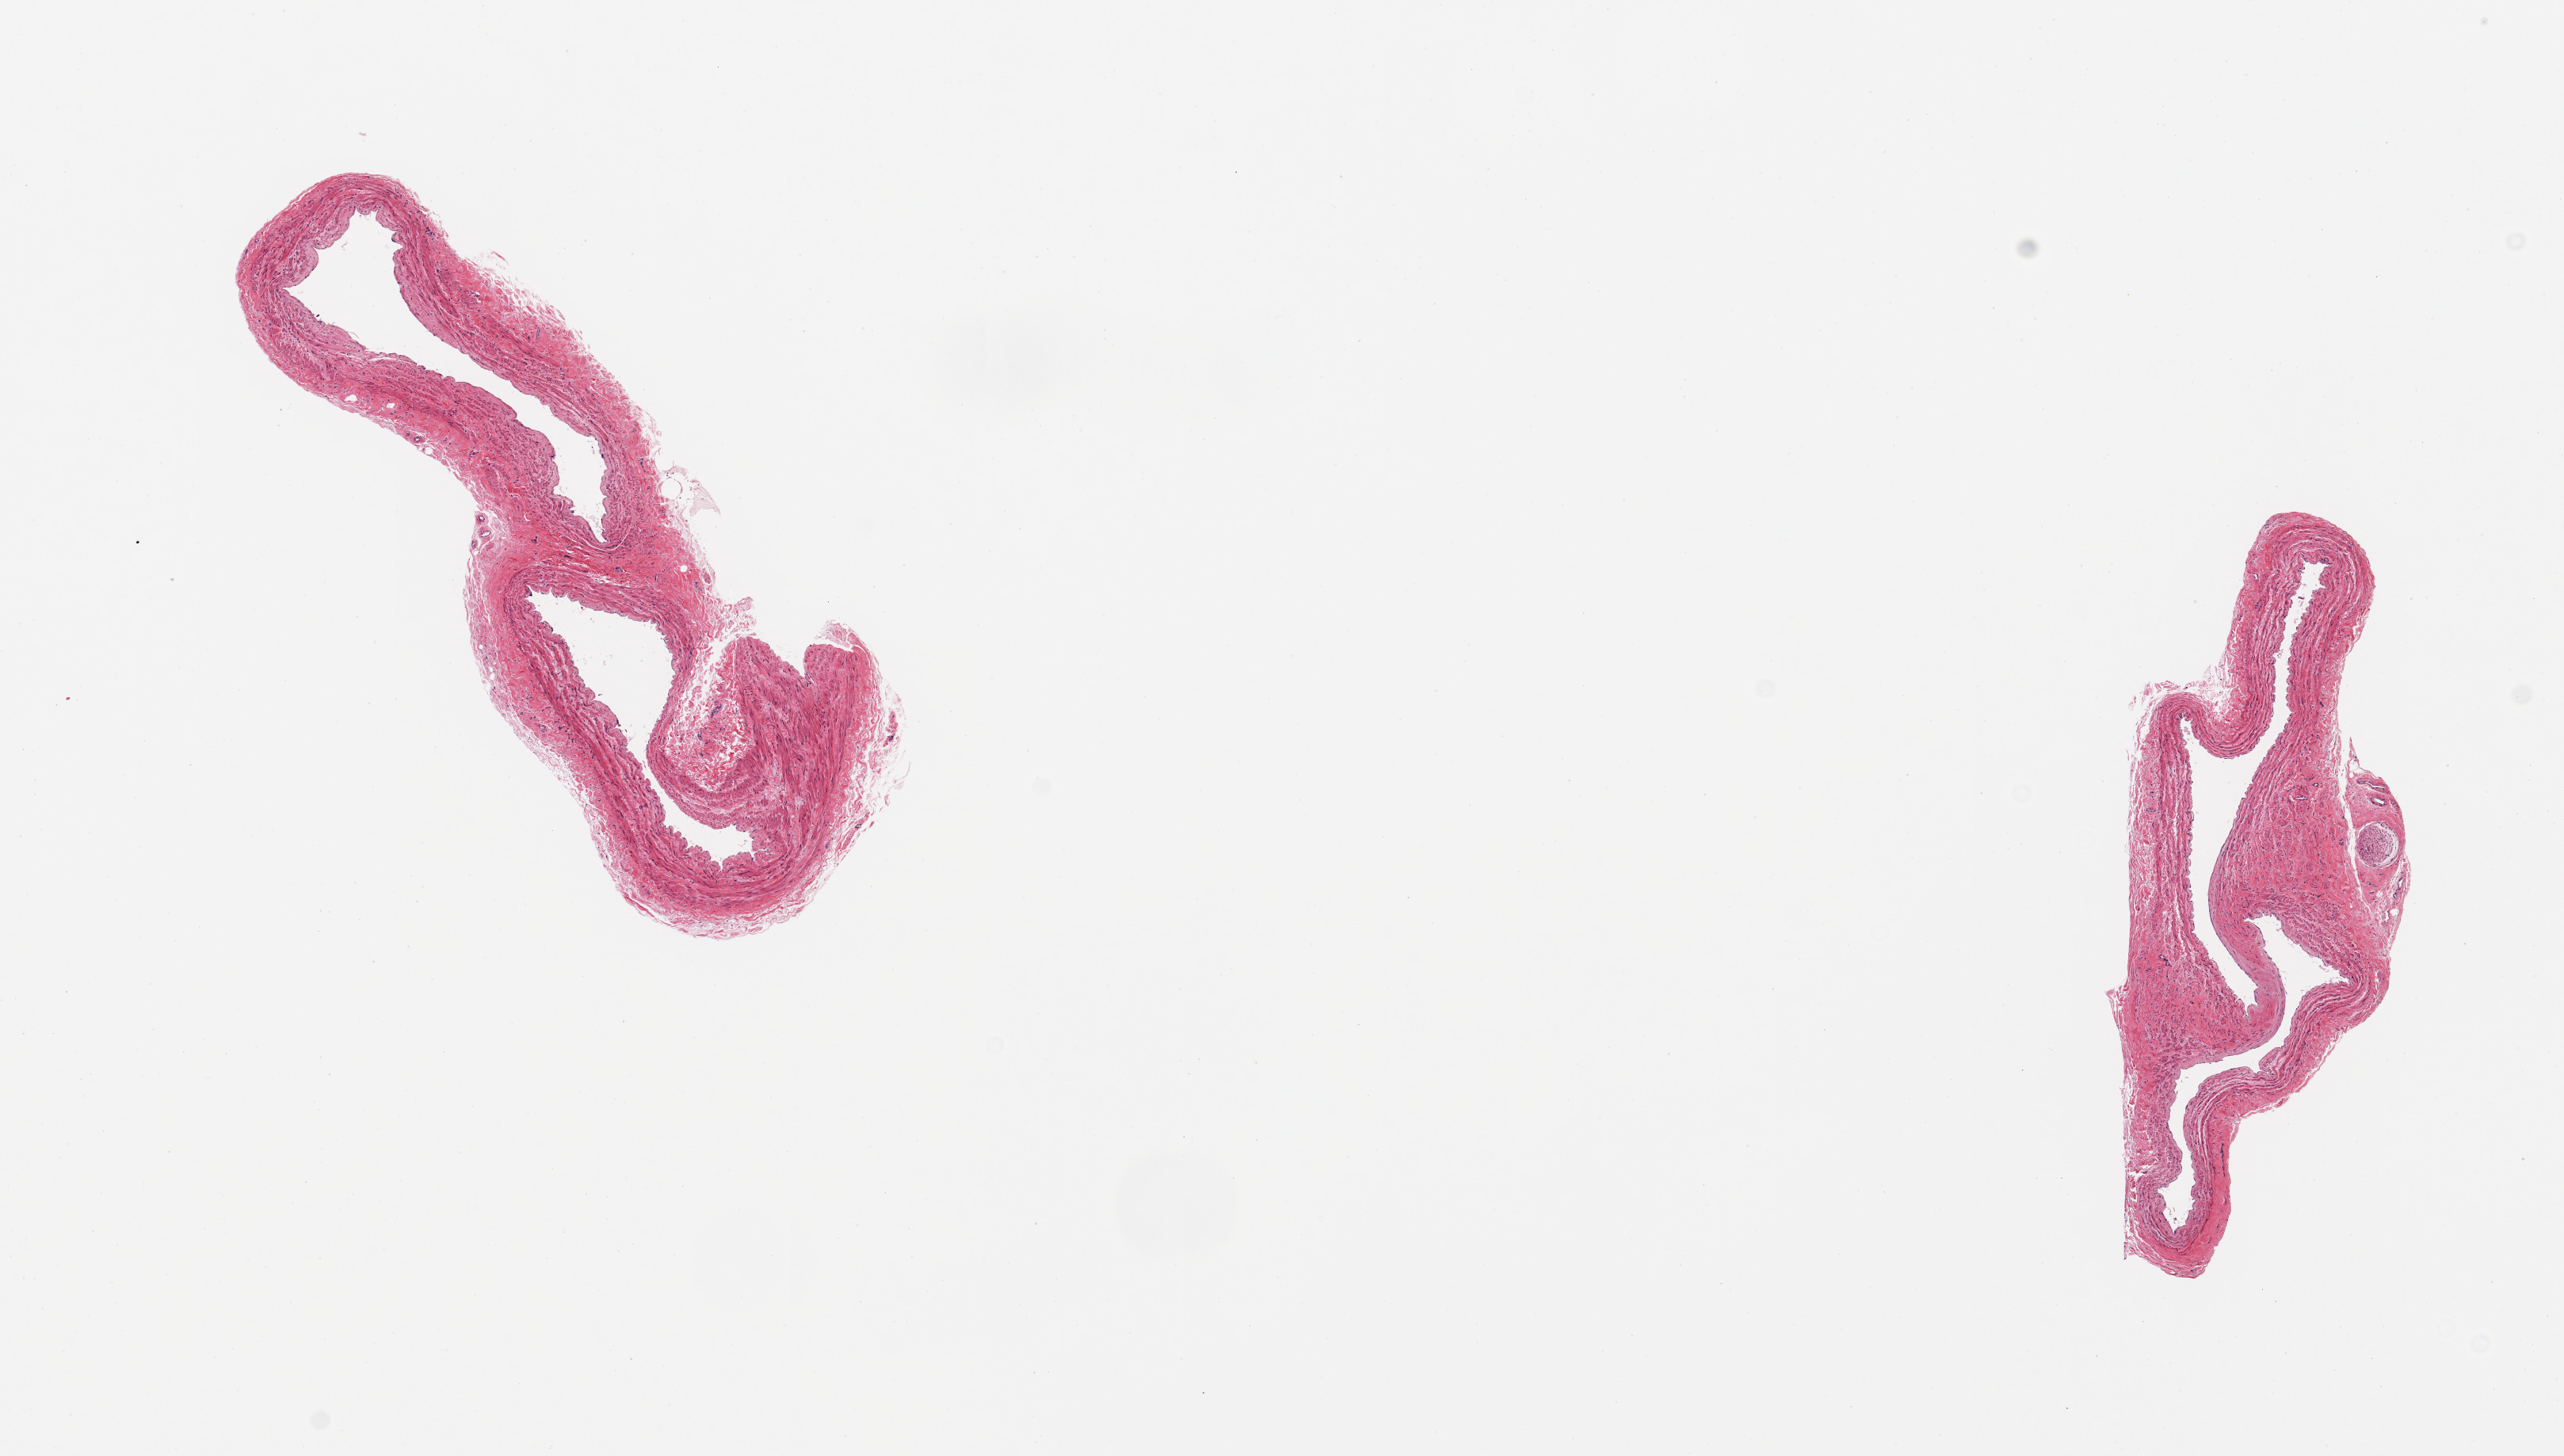
Whole-slide image, hematoxylin and eosin (H&E) stain, brightfield, whole scanned area (about 12.8 x 7.3 mm) shown as a low-resolution overview, PAXgene-fixed paraffin-embedded (PFPE) section, section of tibial artery (target tissue), tissue donor sample.
Review note (as recorded): 2 pieces.